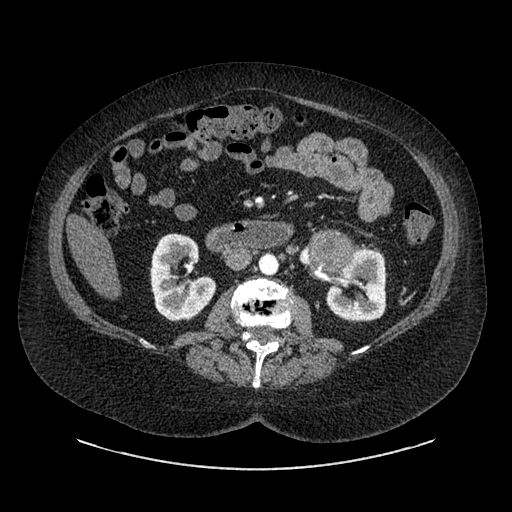
Contrast-enhanced abdominal CT, one axial slice. Slice 491 of 769 in the series (ordered by position). Reconstruction kernel SOFT. 120 kVp. Intravenous contrast given. Soft-tissue window (W 400 / L 40 HU). 0.62 mm slice thickness. 512 × 512 image matrix. Female patient, age 61 years. From the clinical record (not read from this slice): diagnosis: adrenocortical carcinoma; tumour side: left adrenal; tumour size at pathology: 13 cm.
Annotated regions visible in this slice (semi-automatic segmentation, software-assisted and operator-edited):
- mass: bounding box <316,236,349,269> (left, top, right, bottom; pixels)